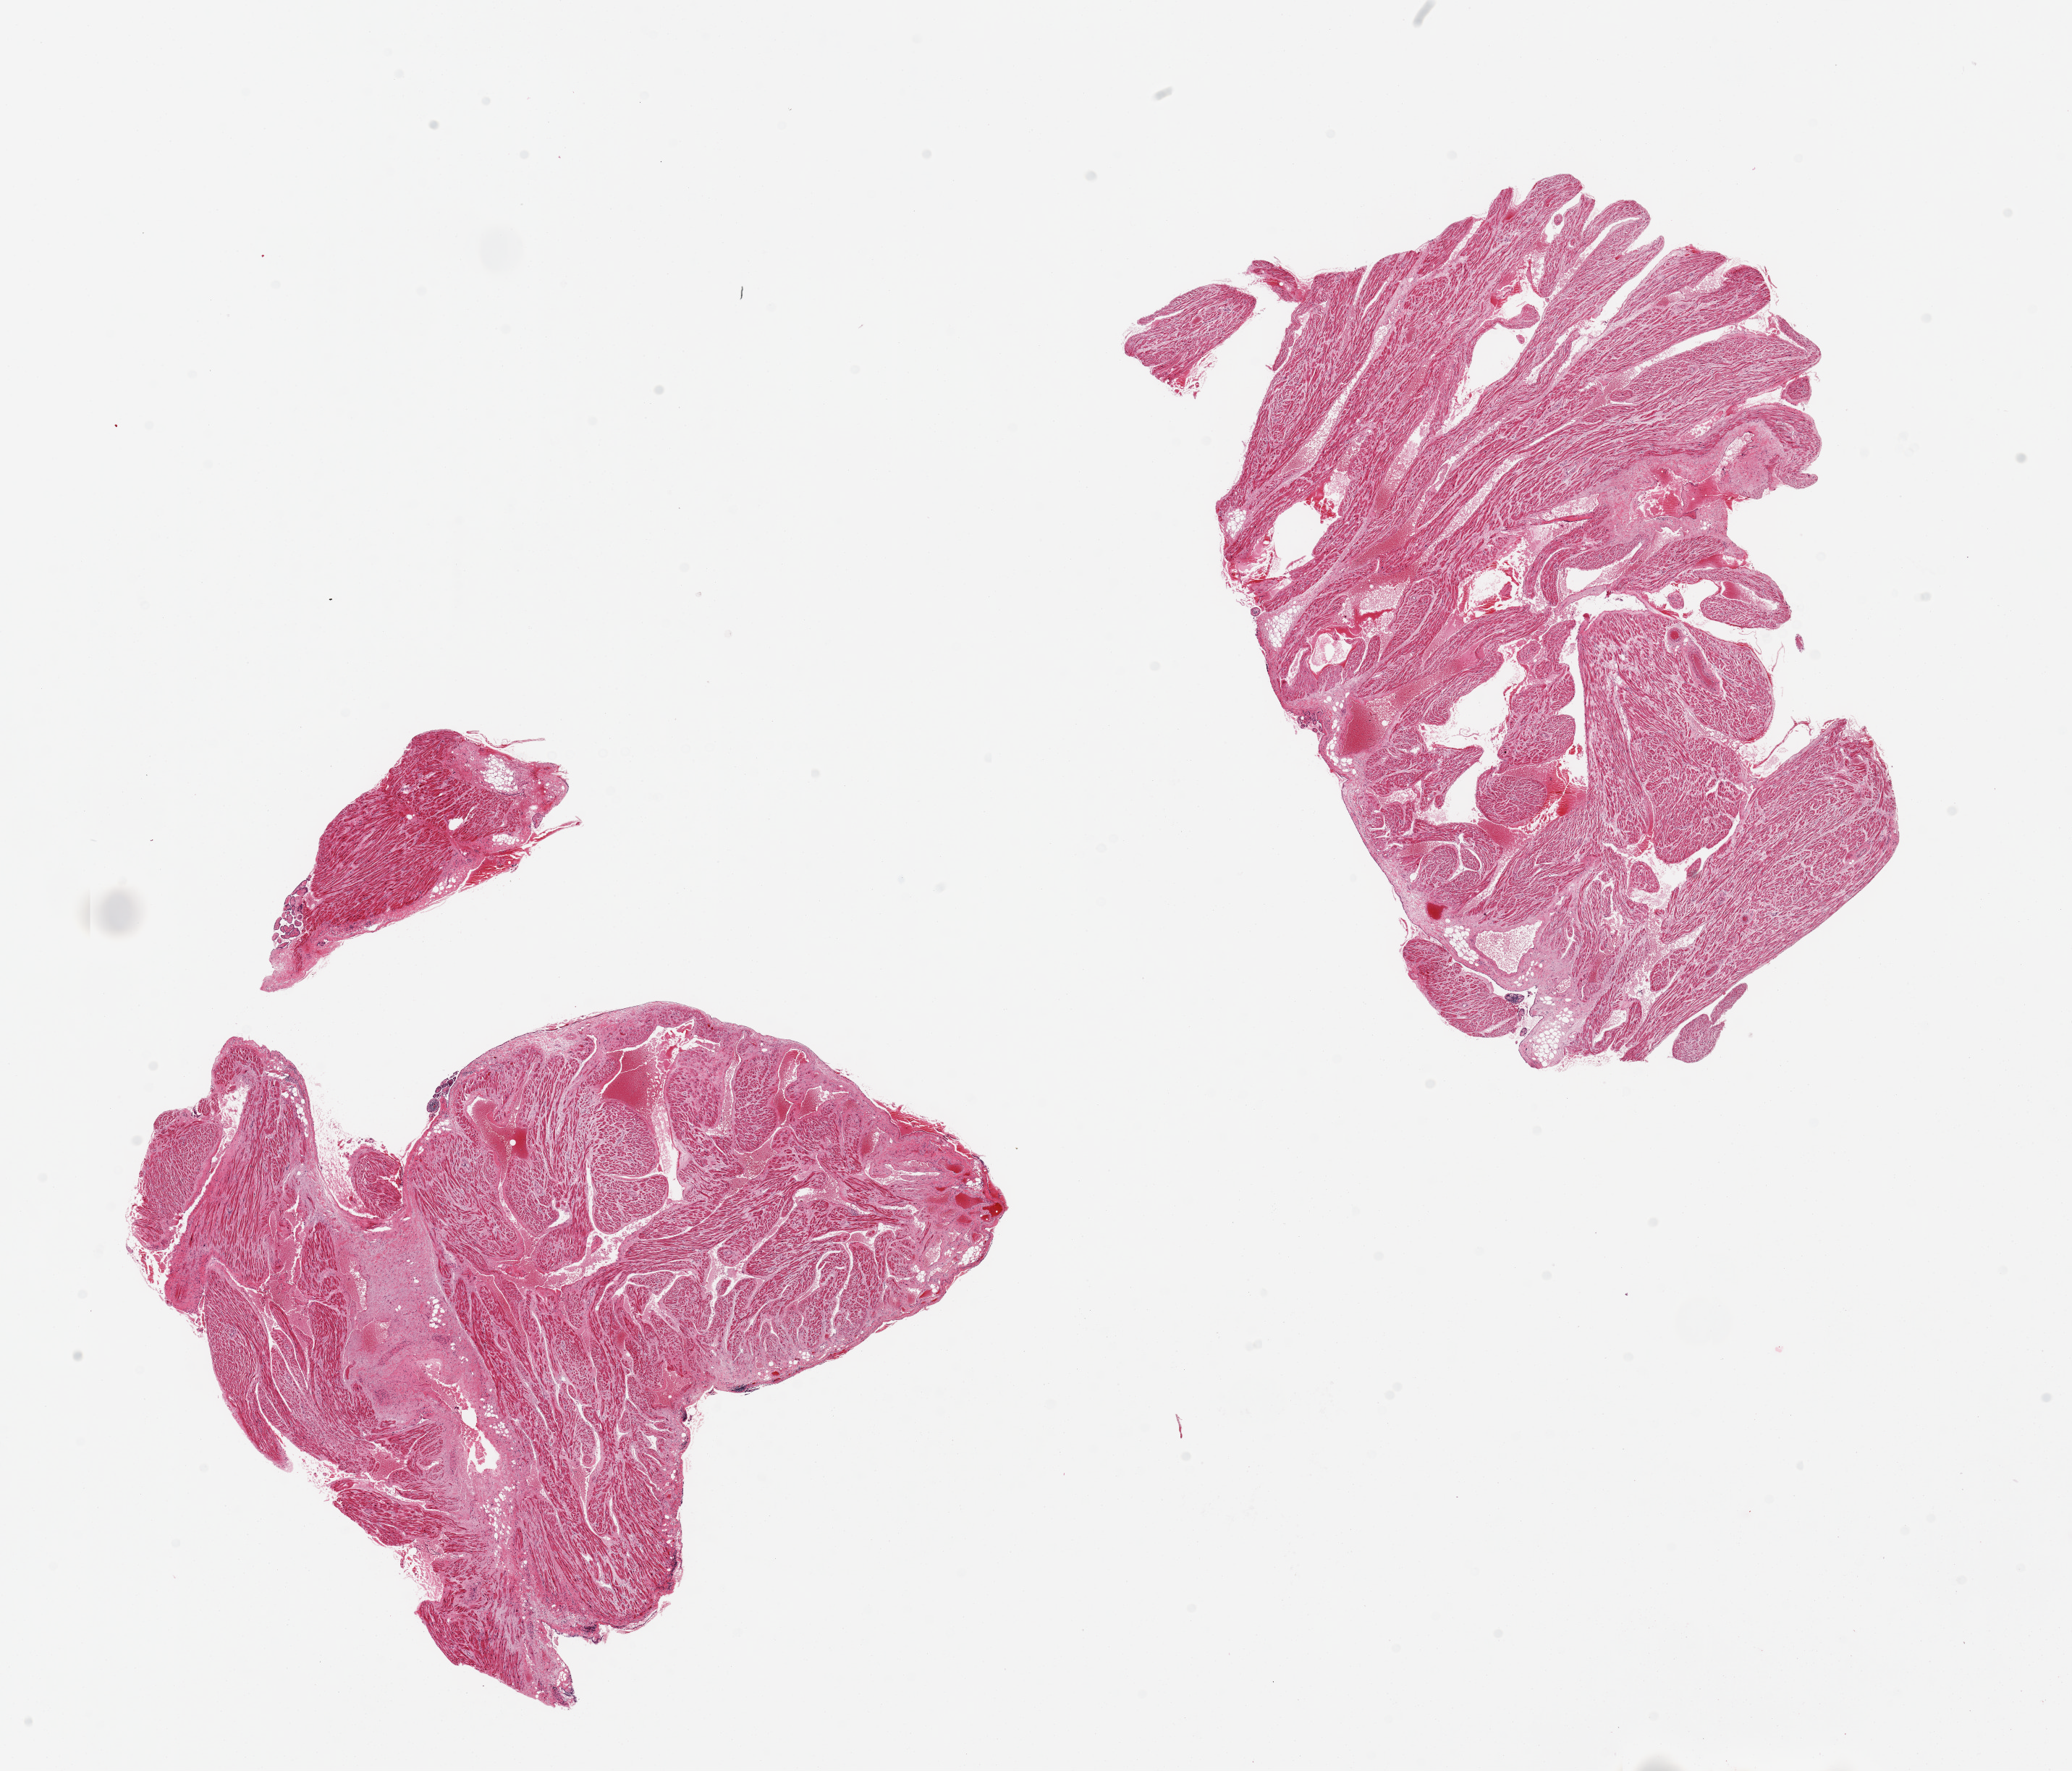
H&E whole-slide image, a low-resolution overview of the entire scanned area, about 22.6 x 19.4 mm (acquisition: 20x scan); PAXgene-fixed, paraffin-embedded tissue; sampled site (target tissue): auricular appendage; donor tissue sample. Male donor.
• review note (as recorded): 2 pieces, 9x7 and 8x7mm